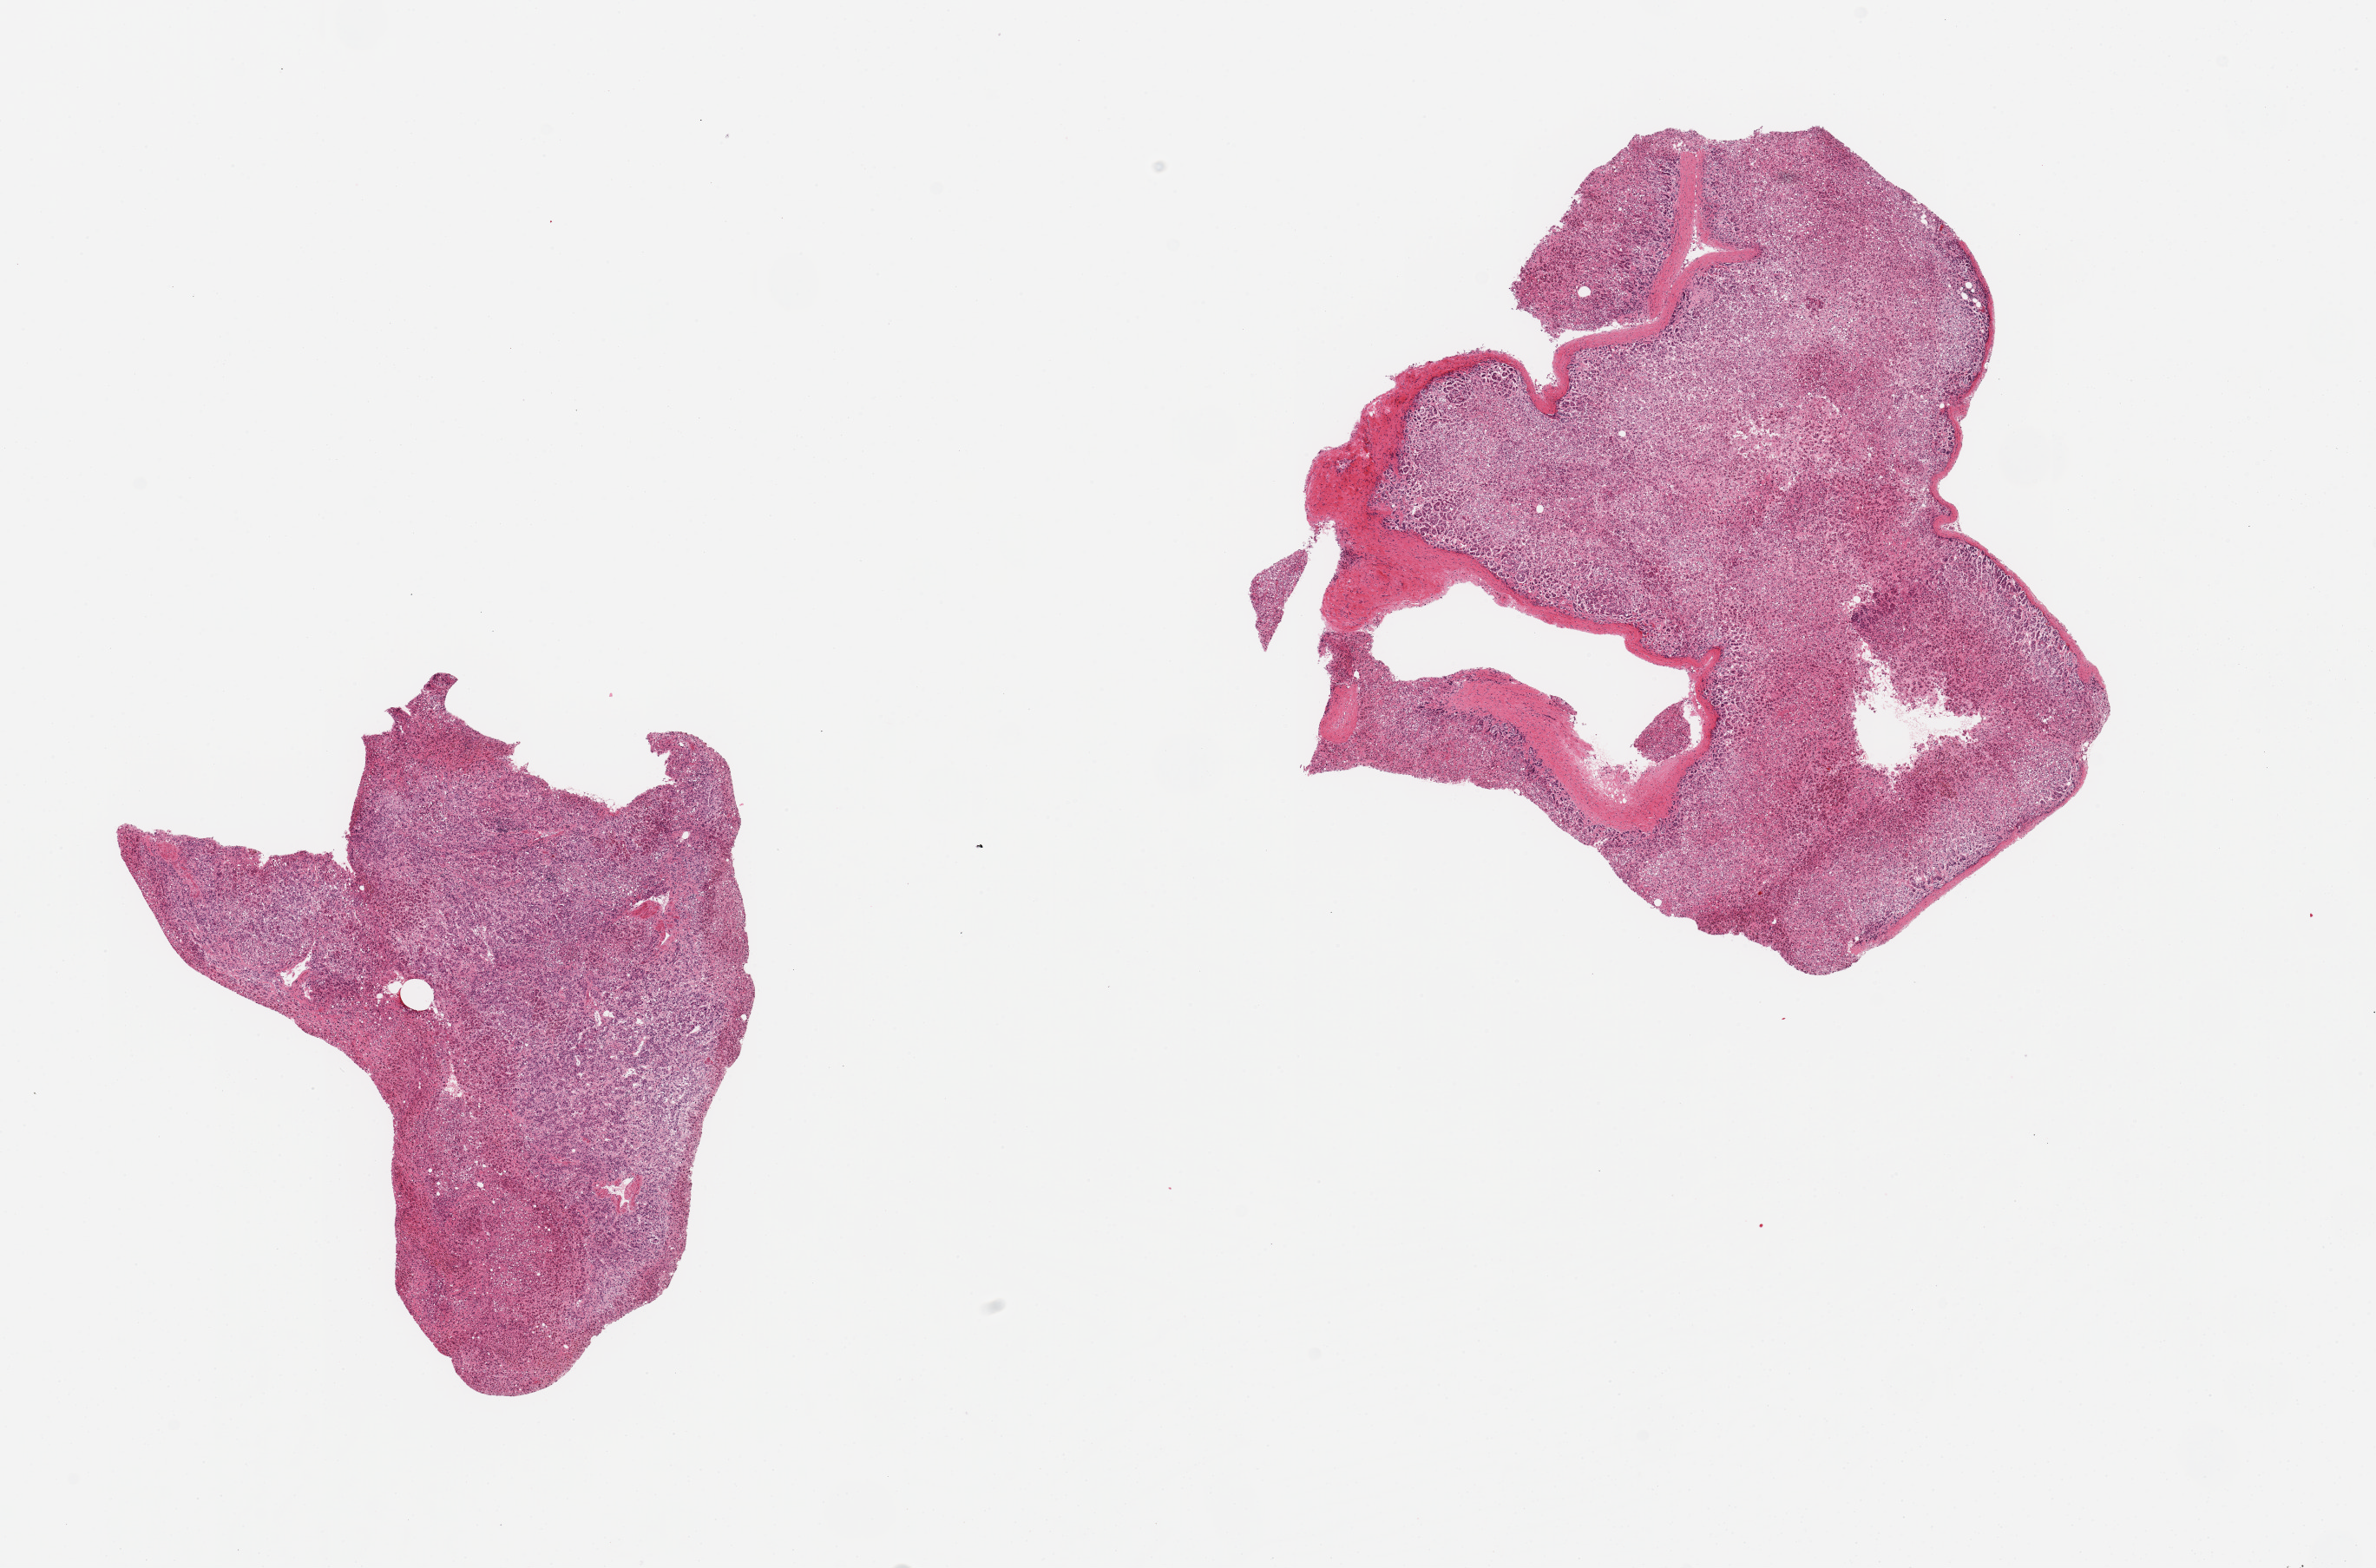
H&E whole-slide image, whole scanned area (about 21.7 x 14.3 mm, from a 20x scan) shown as a low-resolution overview, PAXgene-fixed paraffin-embedded (PFPE) section, target tissue: adrenal gland, donor tissue sample. Donor sex: female.
- reviewer comment on this tissue sample: 2 pieces